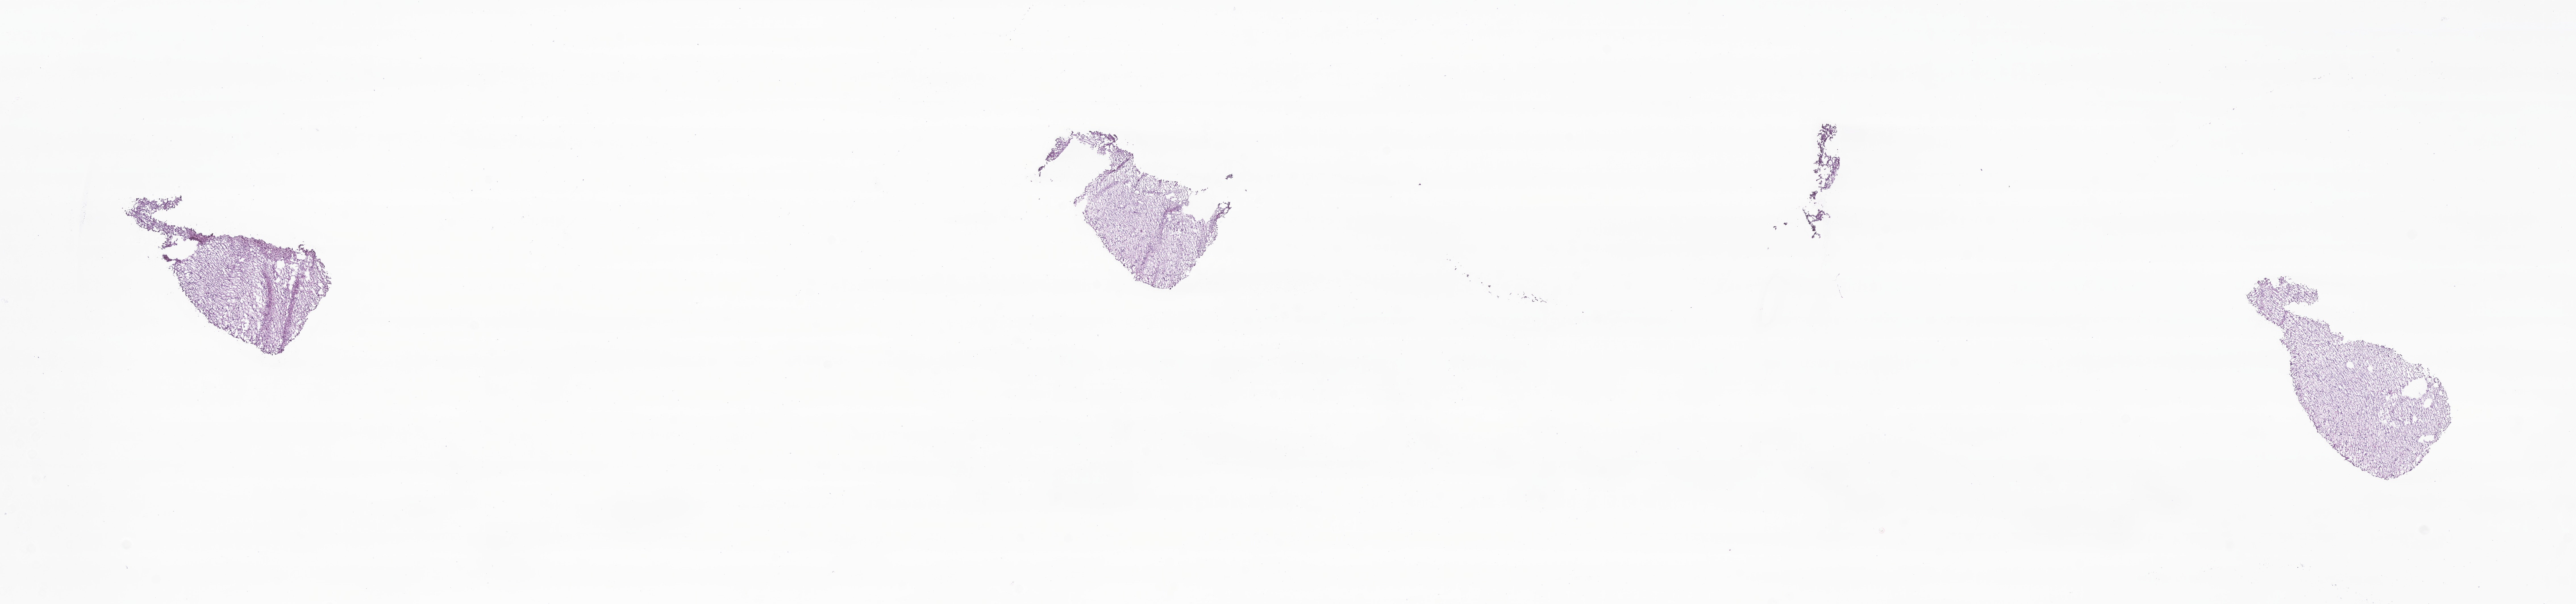
Hematoxylin and eosin (H&E) whole-slide image of tumor tissue from the parietal lobe — a low-resolution overview of the entire scanned area, about 38.2 x 9.0 mm, cryosection (OCT / tissue freezing medium). Female patient, age 202 months.
* diagnosis (ICD-O-3 morphology term): Glioma, malignant